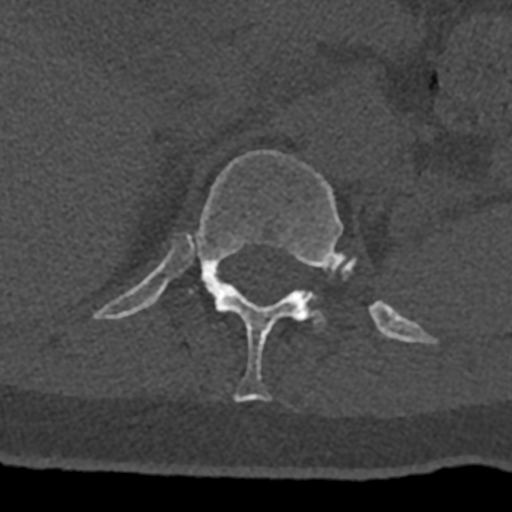
CT including the spine, one axial slice; position 488 of 797 along the scan axis; reconstruction kernel Br40s/3; bone window (W 1800 / L 400 HU); 0.5 mm slice thickness; 512 × 512 image matrix, field of view 160 × 160 mm. Patient: male, 74 years. Case-level facts recorded for this patient, not image findings: primary cancer: renal.
Structures marked on this image (semi-automatic segmentation, software-assisted and operator-edited):
- L1 vertebra: bounding box [x1, y1, x2, y2] px = [307, 295, 326, 324]
- T12 vertebra: [93, 150, 432, 402]